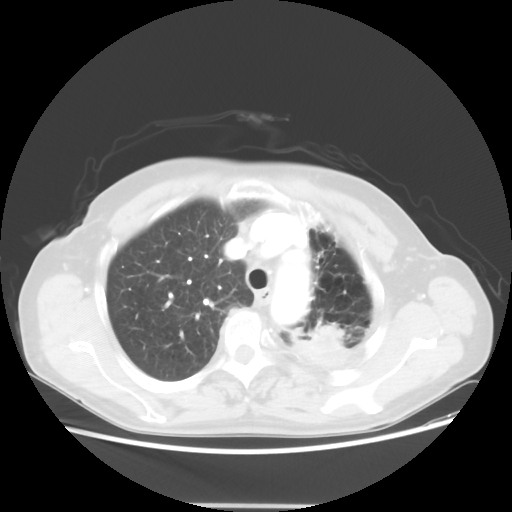
Chest CT, one axial slice; position 41 of 56 along the scan axis; 100 kVp; lung window (W 1500 / L -600 HU); 512 × 512 image matrix, field of view 377 × 377 mm. Patient: female, 63 years. Case-level facts recorded for this patient, not image findings: clinical TNM (as recorded): T2a N0 M0.
Structures marked on this image (rectangle marked by the reading radiologist):
- lung tumour (recorded histology: adenocarcinoma): bounding box <302,321,348,369> (left, top, right, bottom; pixels)